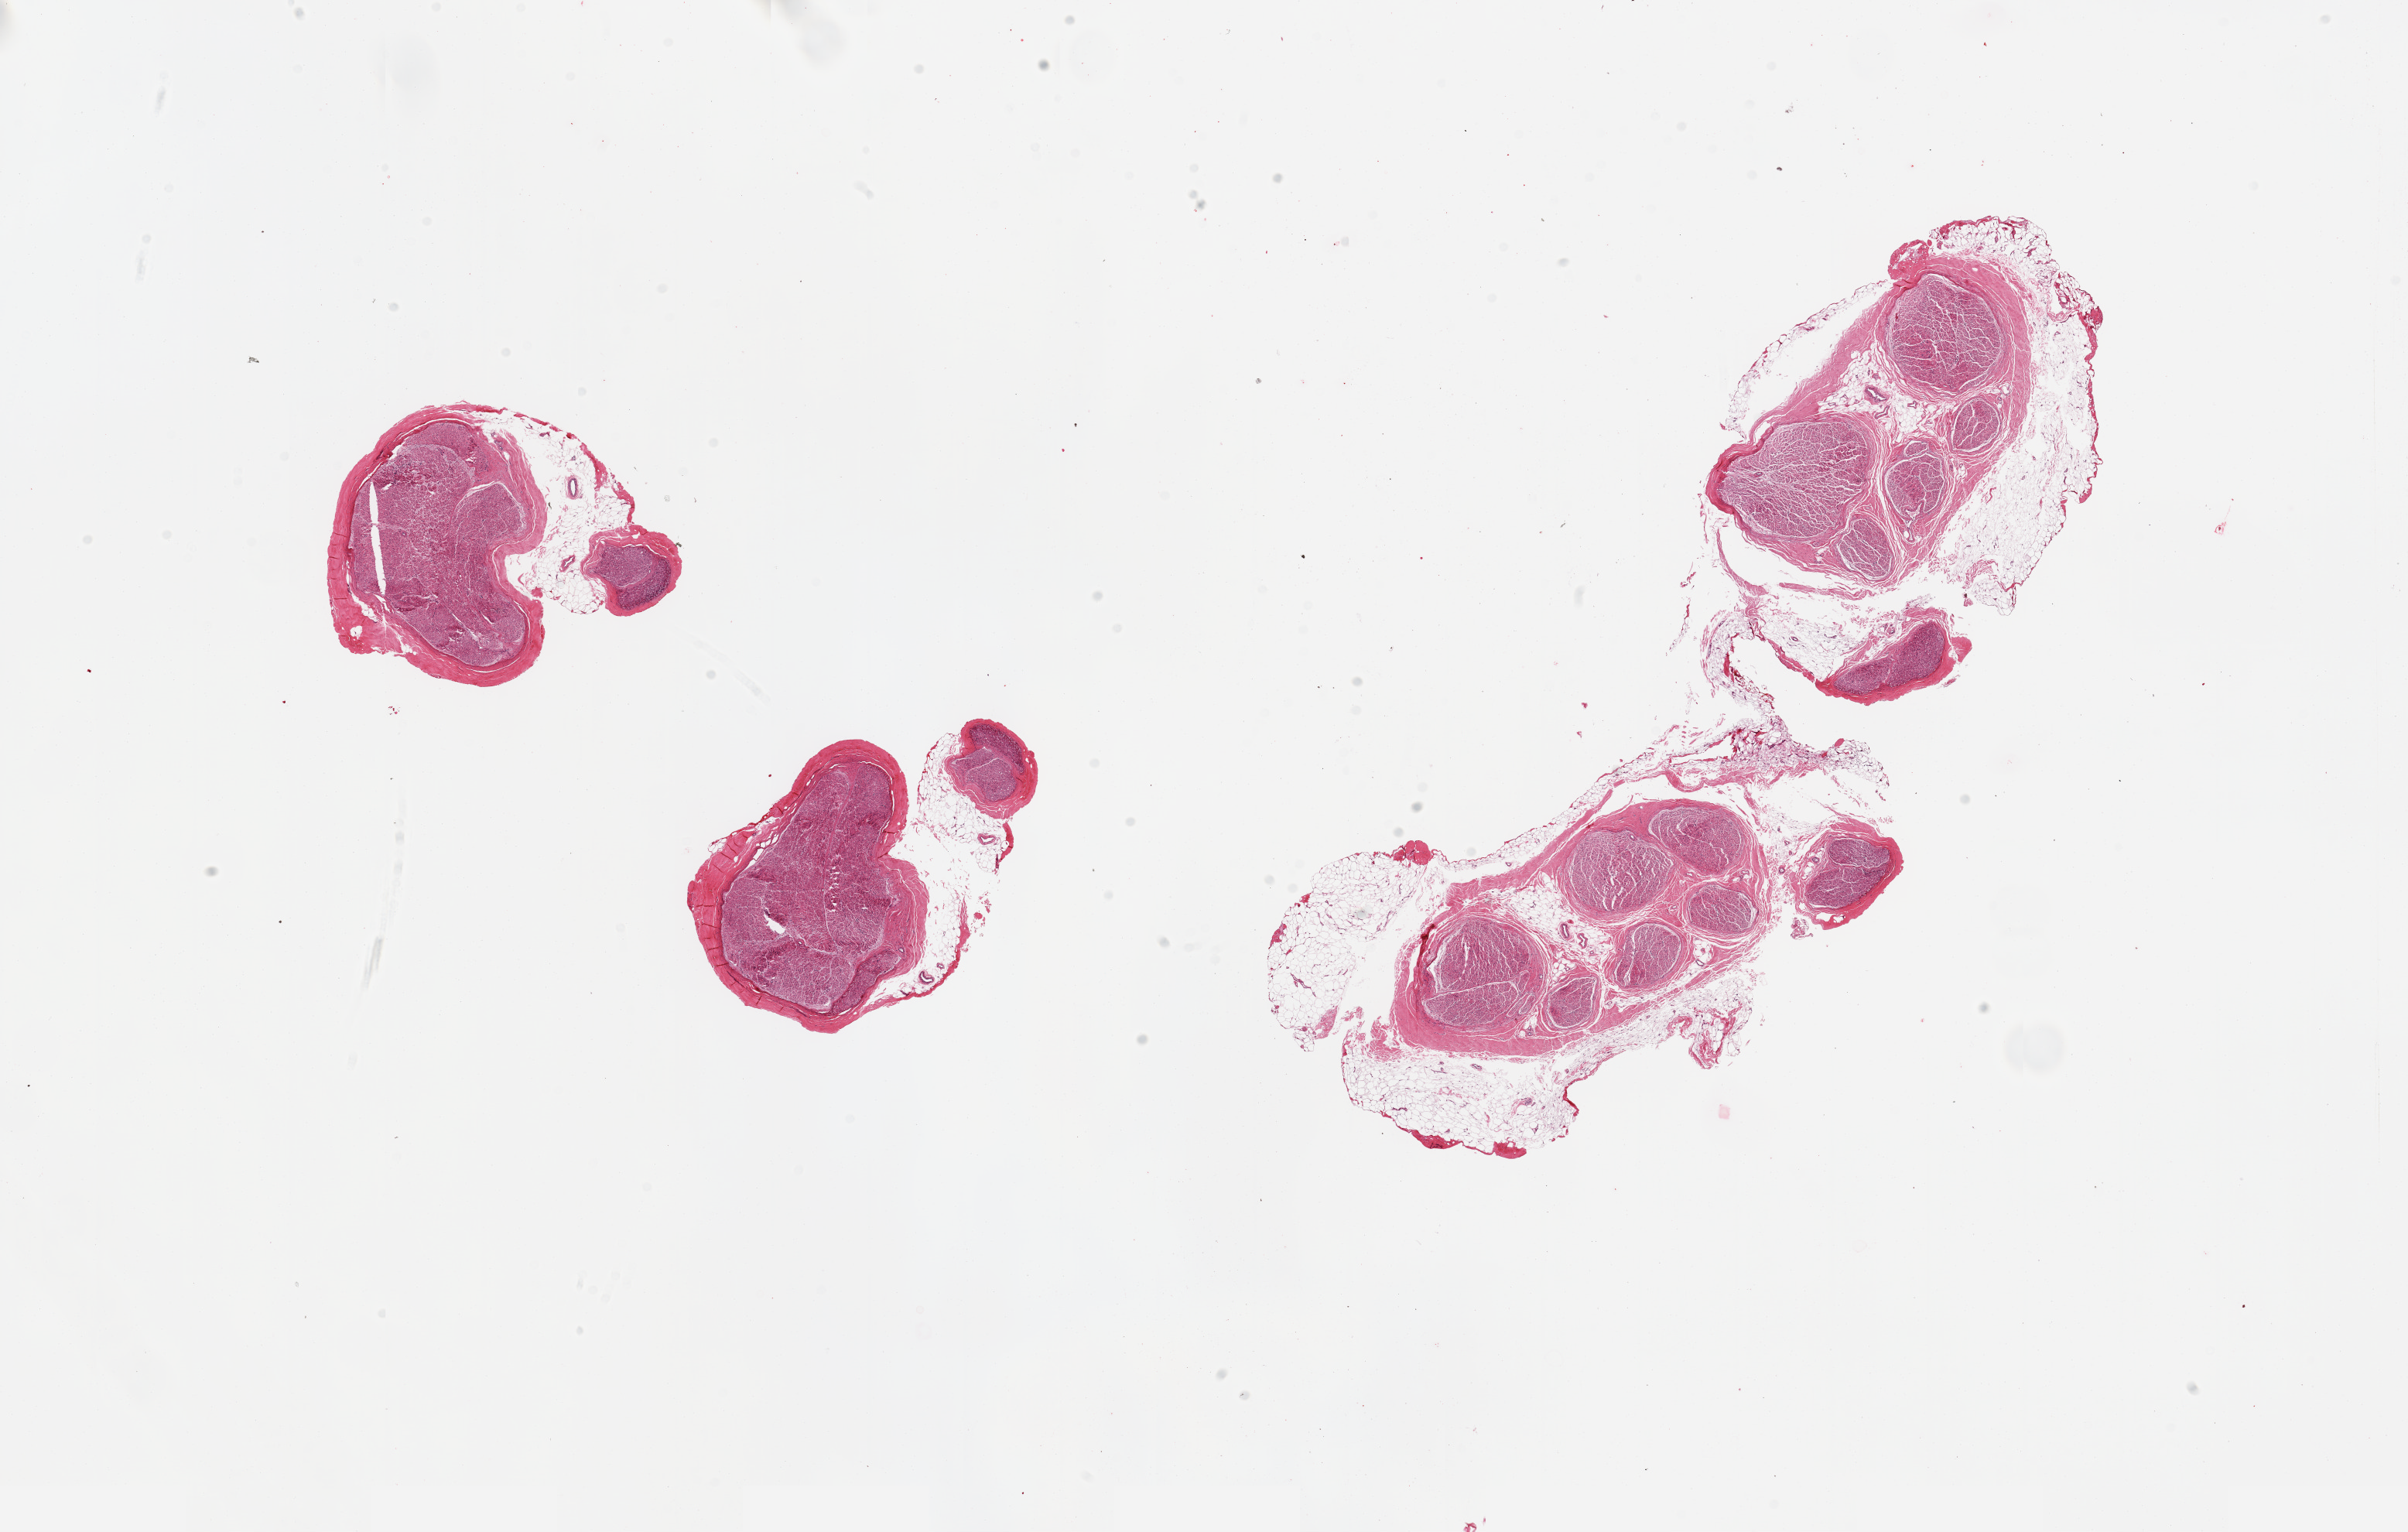
Haematoxylin and eosin whole-slide image — a low-resolution overview of the entire scanned area, about 24.6 x 15.7 mm (from a 20x scan); PAXgene-fixed, paraffin-embedded tissue; sampled site (target tissue): tibial nerve; donor tissue sample. Male donor.
Reviewer comment on this tissue sample: 3 pieces; surrounding fat up to 1mm.